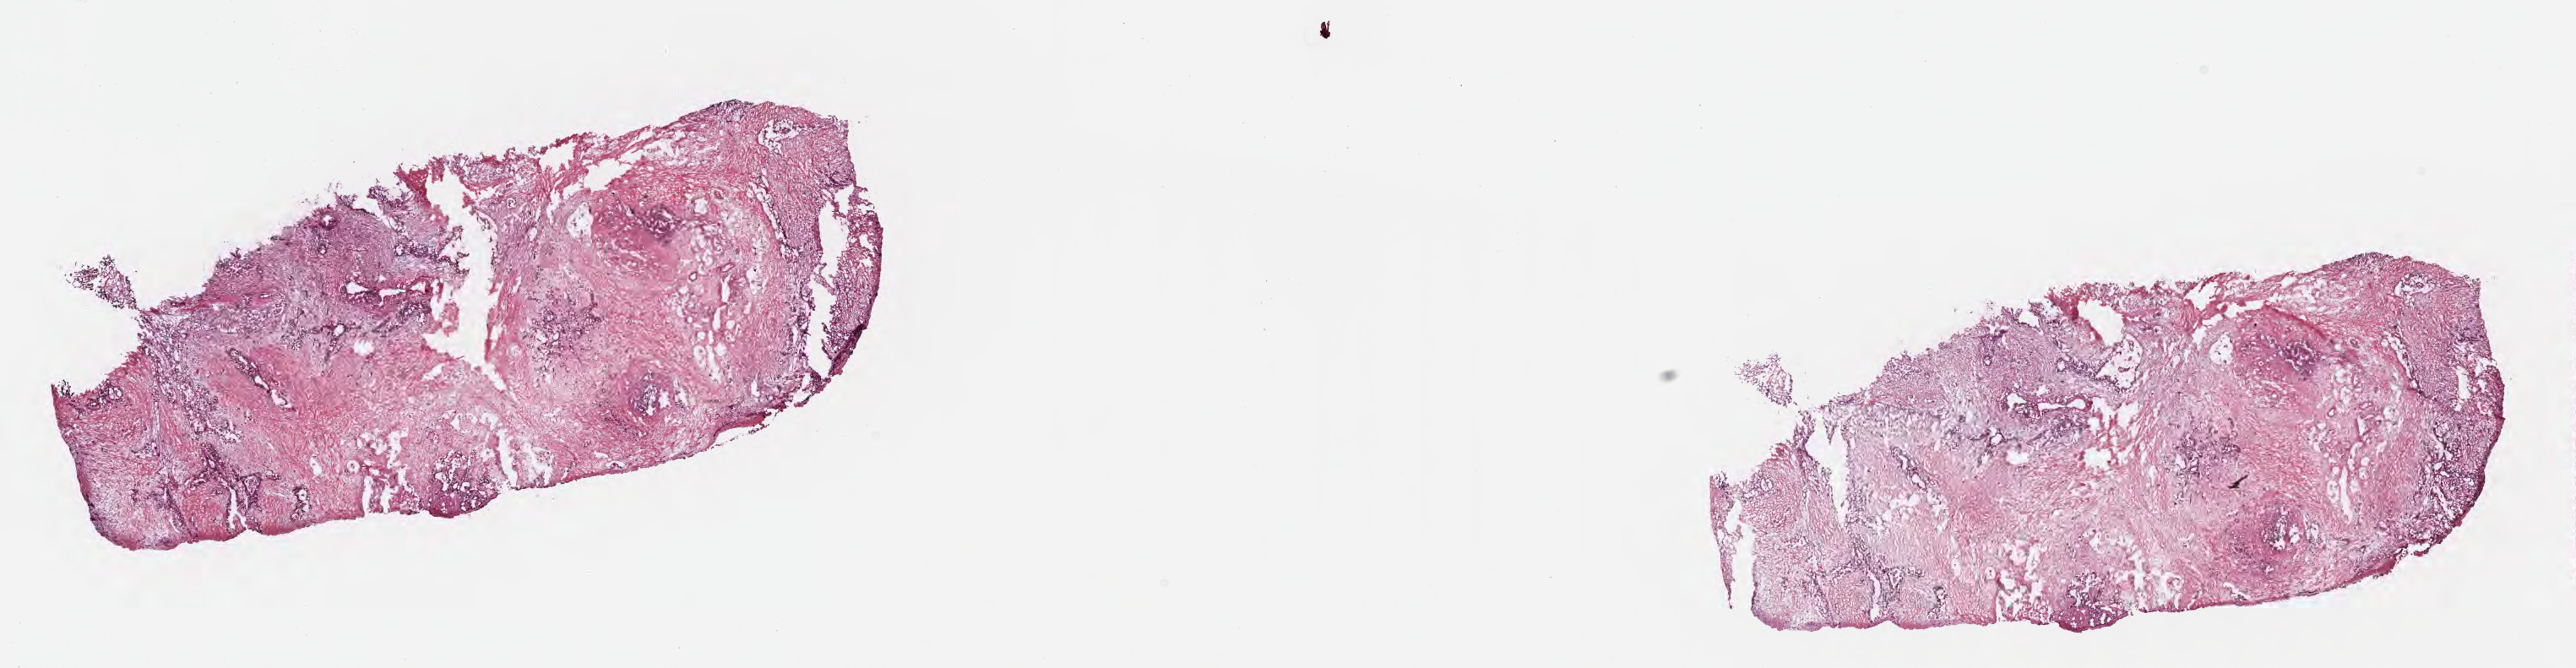
Hematoxylin and eosin (H&E) whole-slide image — low-resolution overview of the scanned area, about 24.6 x 6.4 mm; frozen section; specimen: primary tumor; anatomic site: body of pancreas. Female, age 74 years at initial diagnosis. Tumor grade: G2 (moderately differentiated). Slide review estimates, as recorded: tumor cells 50%, tumor nuclei 50%, stromal cells 20%, necrosis 5%, normal cells 25%. Infiltration values recorded for this section: lymphocyte infiltration 6%, monocyte infiltration 1%, neutrophil infiltration 7%.
Section: top of the tissue portion. Histologic diagnosis: Infiltrating duct carcinoma, NOS. AJCC pathologic stage: Stage IIB.